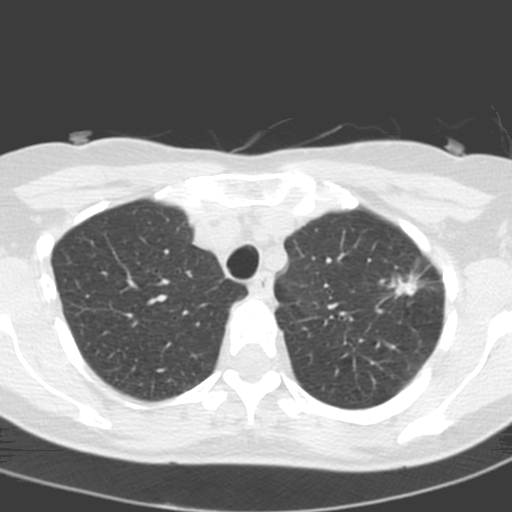
Axial slice from a low-dose chest CT screening exam; baseline annual screen; lung window (W 1500 / L -600 HU); standard (soft-tissue) reconstruction kernel (C); 120 kVp; slice 40 of 193 in the series. Female, age 58 years at enrolment. Current smoker at enrolment.
• Expert reader's lesion annotation, bounding box (x1, y1, x2, y2) in pixels: (379, 263, 431, 314).
• Screening reader's record for this exam (one nodule recorded; not confirmed to be the boxed lesion): non-calcified nodule or mass ≥4 mm, left upper lobe, 14 × 10 mm, spiculated (stellate) margins, soft tissue attenuation.
• Official screen result: positive, change unspecified: nodule(s) >= 4 mm or enlarging nodule(s), mass(es), or other non-specific abnormalities suspicious for lung cancer.
• Later outcome: lung cancer diagnosed 48 days after this screen — adenocarcinoma, NOS, left upper lobe, poorly differentiated (G3), stage IA (AJCC 6th edition), 13 mm at pathology.